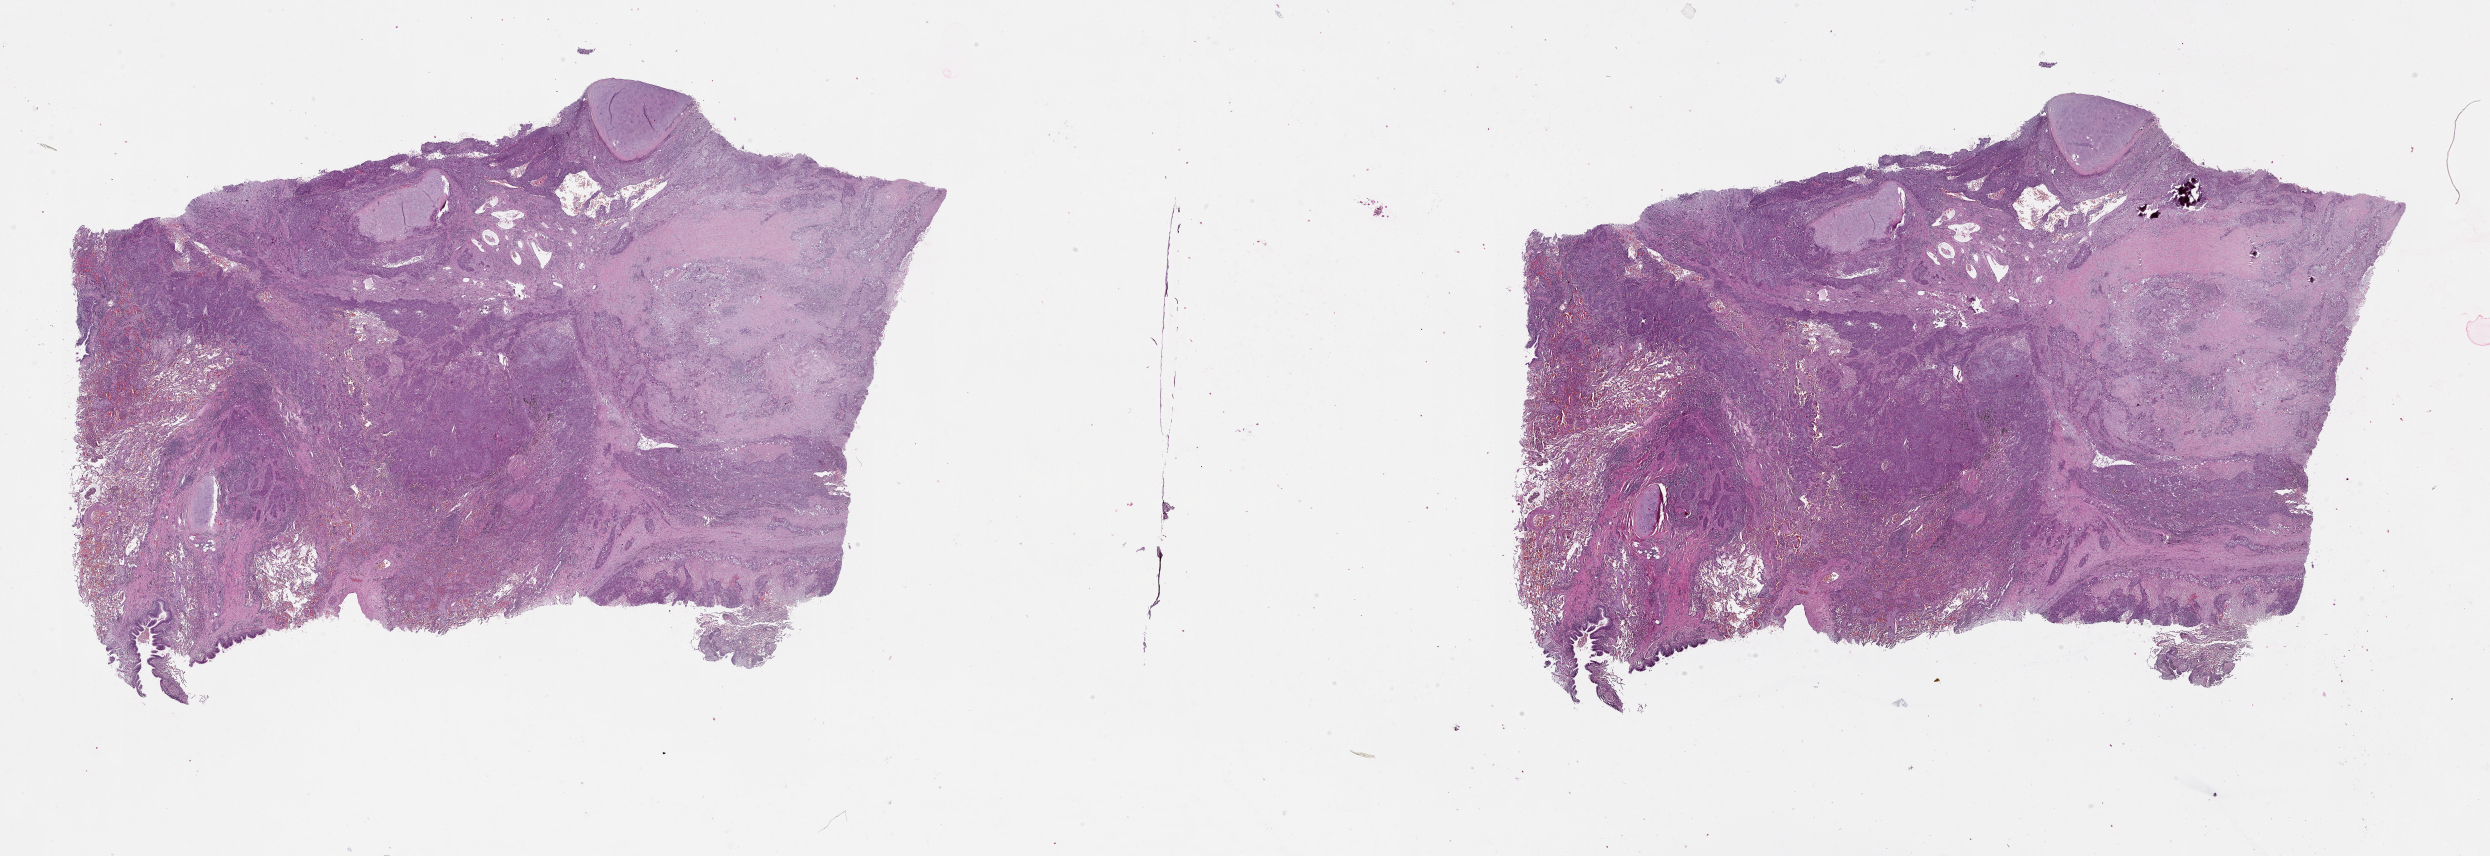
Digitized Hematoxylin and eosin (H&E) stained tissue section (whole slide), low-resolution overview of the scanned area, about 40.1 x 13.8 mm, lung, tumour tissue. Male, 58 y/o.
Patient diagnosis (cohort enrolment): squamous cell carcinoma (lung).